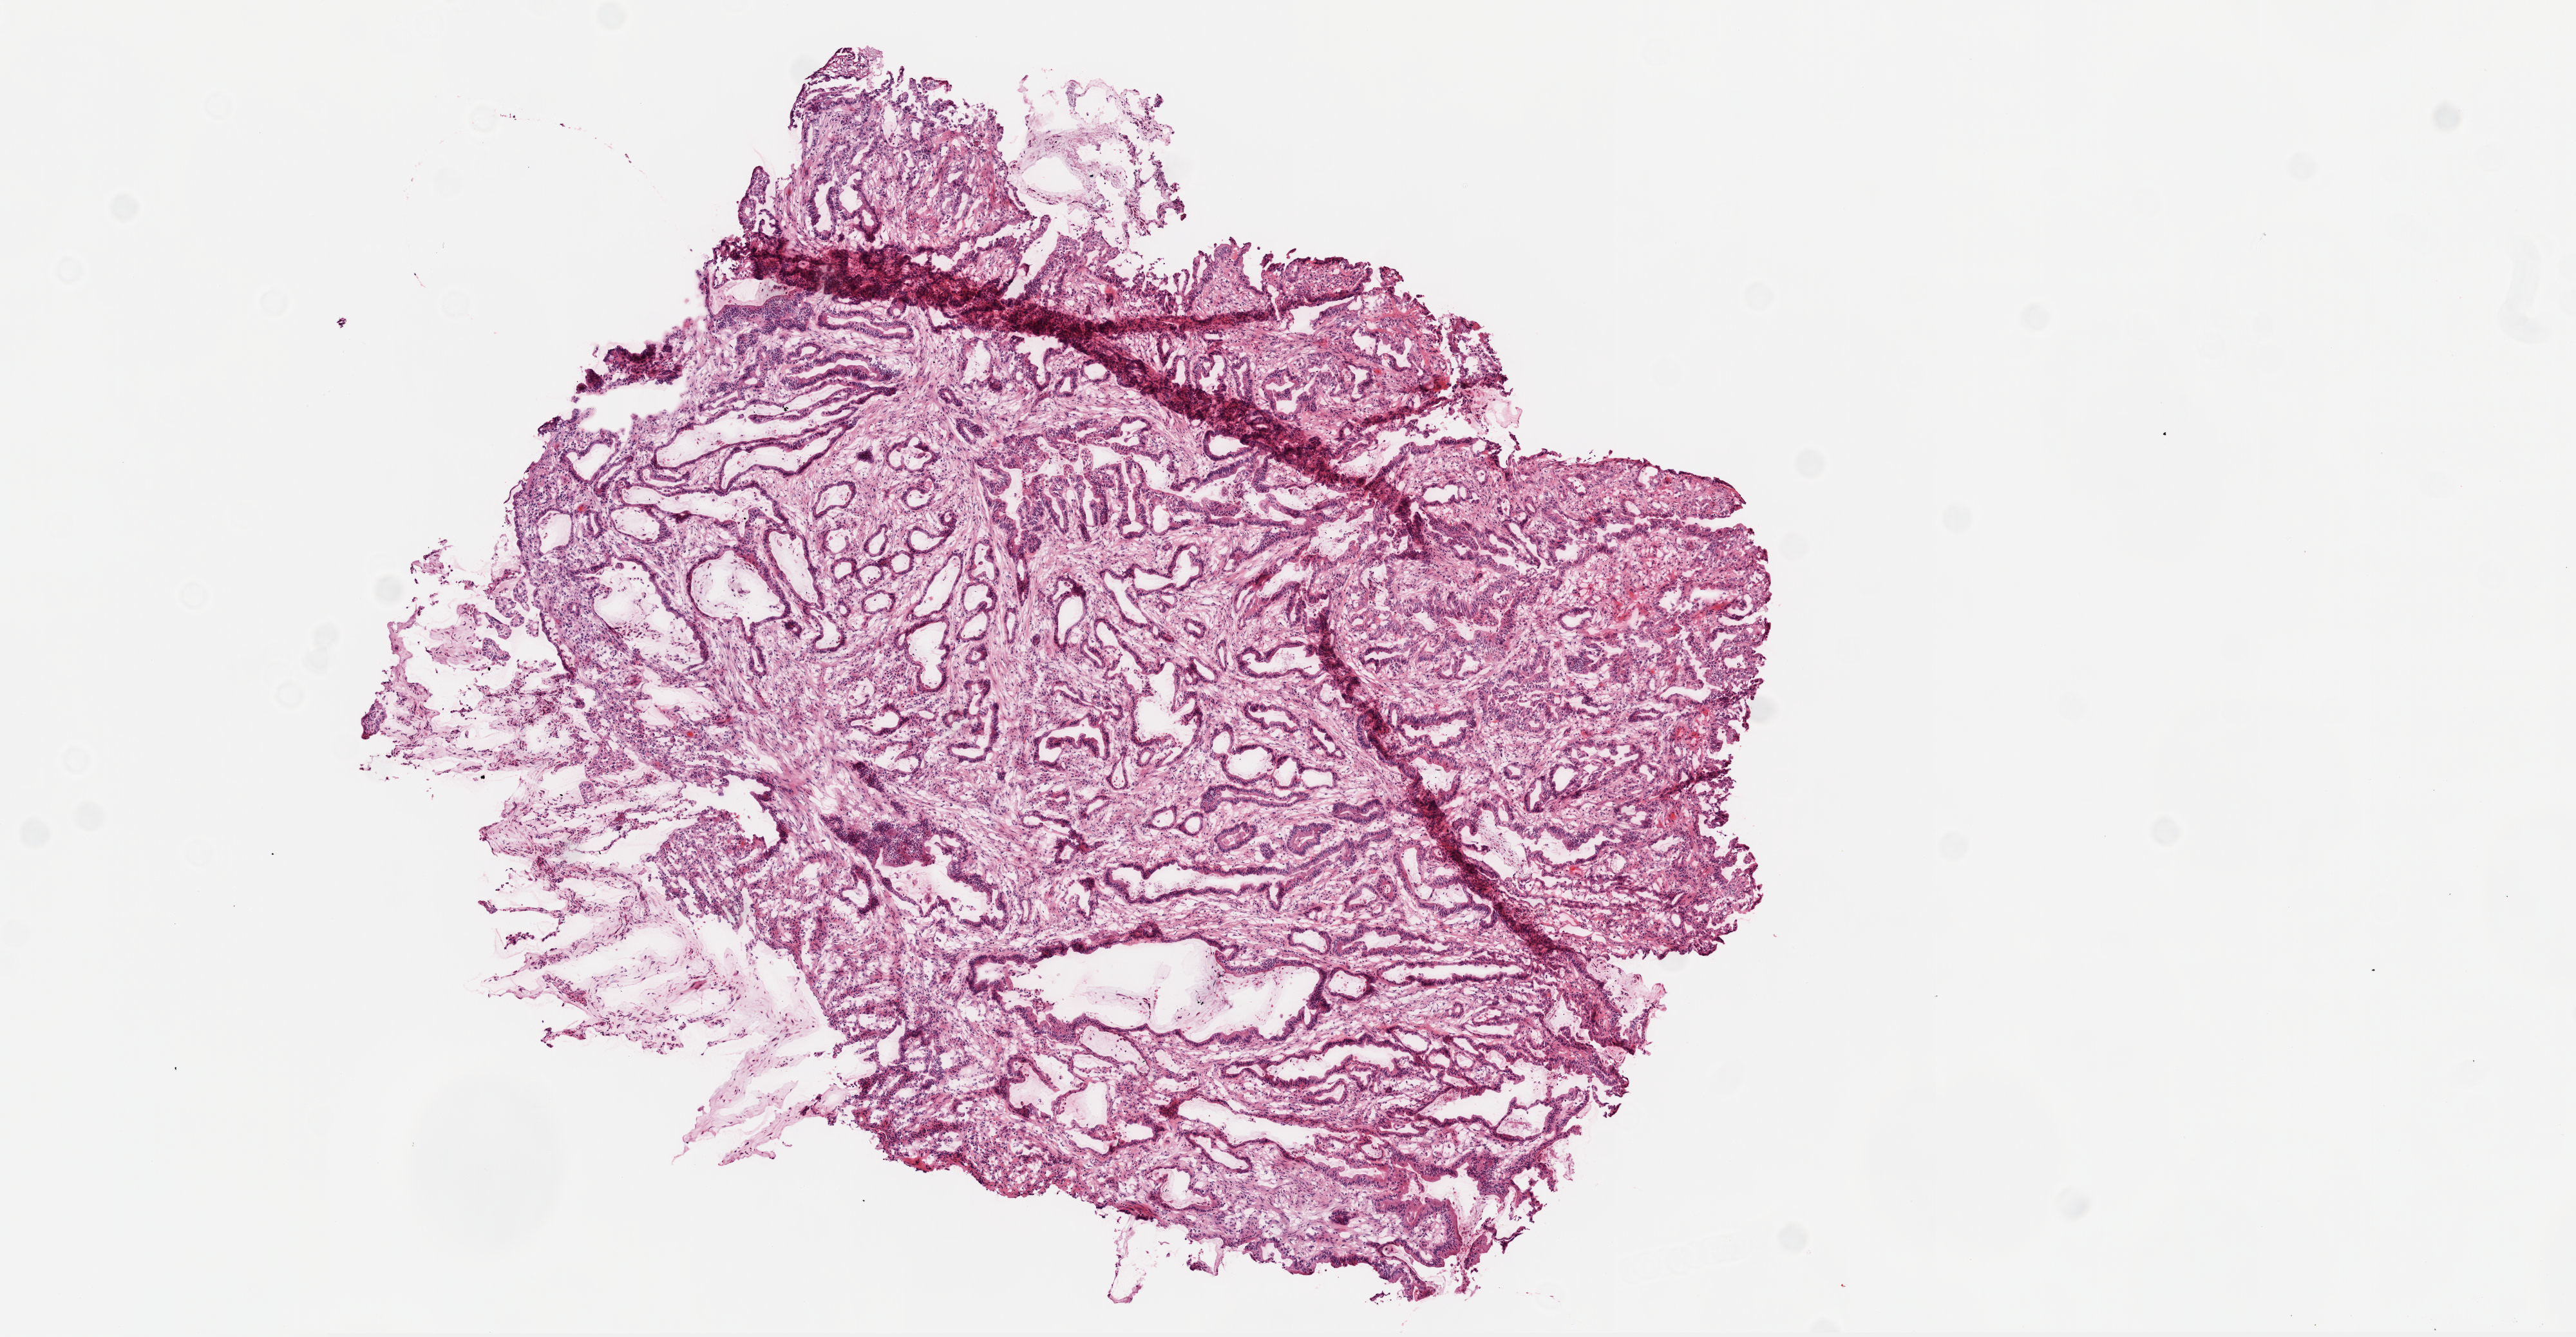
Digitized H&E tissue section (whole slide) — whole scanned area (about 8.0 x 4.2 mm, from a 20x scan) shown as a low-resolution overview; frozen section from the top of the tissue portion; colon, primary tumour sample. Female, age 79 years at initial diagnosis. Slide review estimates, as recorded: tumour cells 80%, tumour nuclei 75%, normal cells 5%, stromal cells 15%, necrosis 0%.
• TNM: T3 N0 M0
• lymph nodes positive (case pathology): 0 of 30 examined
• AJCC pathologic stage: IIA (6th edition)
• diagnosis: Mucinous adenocarcinoma (cecum)